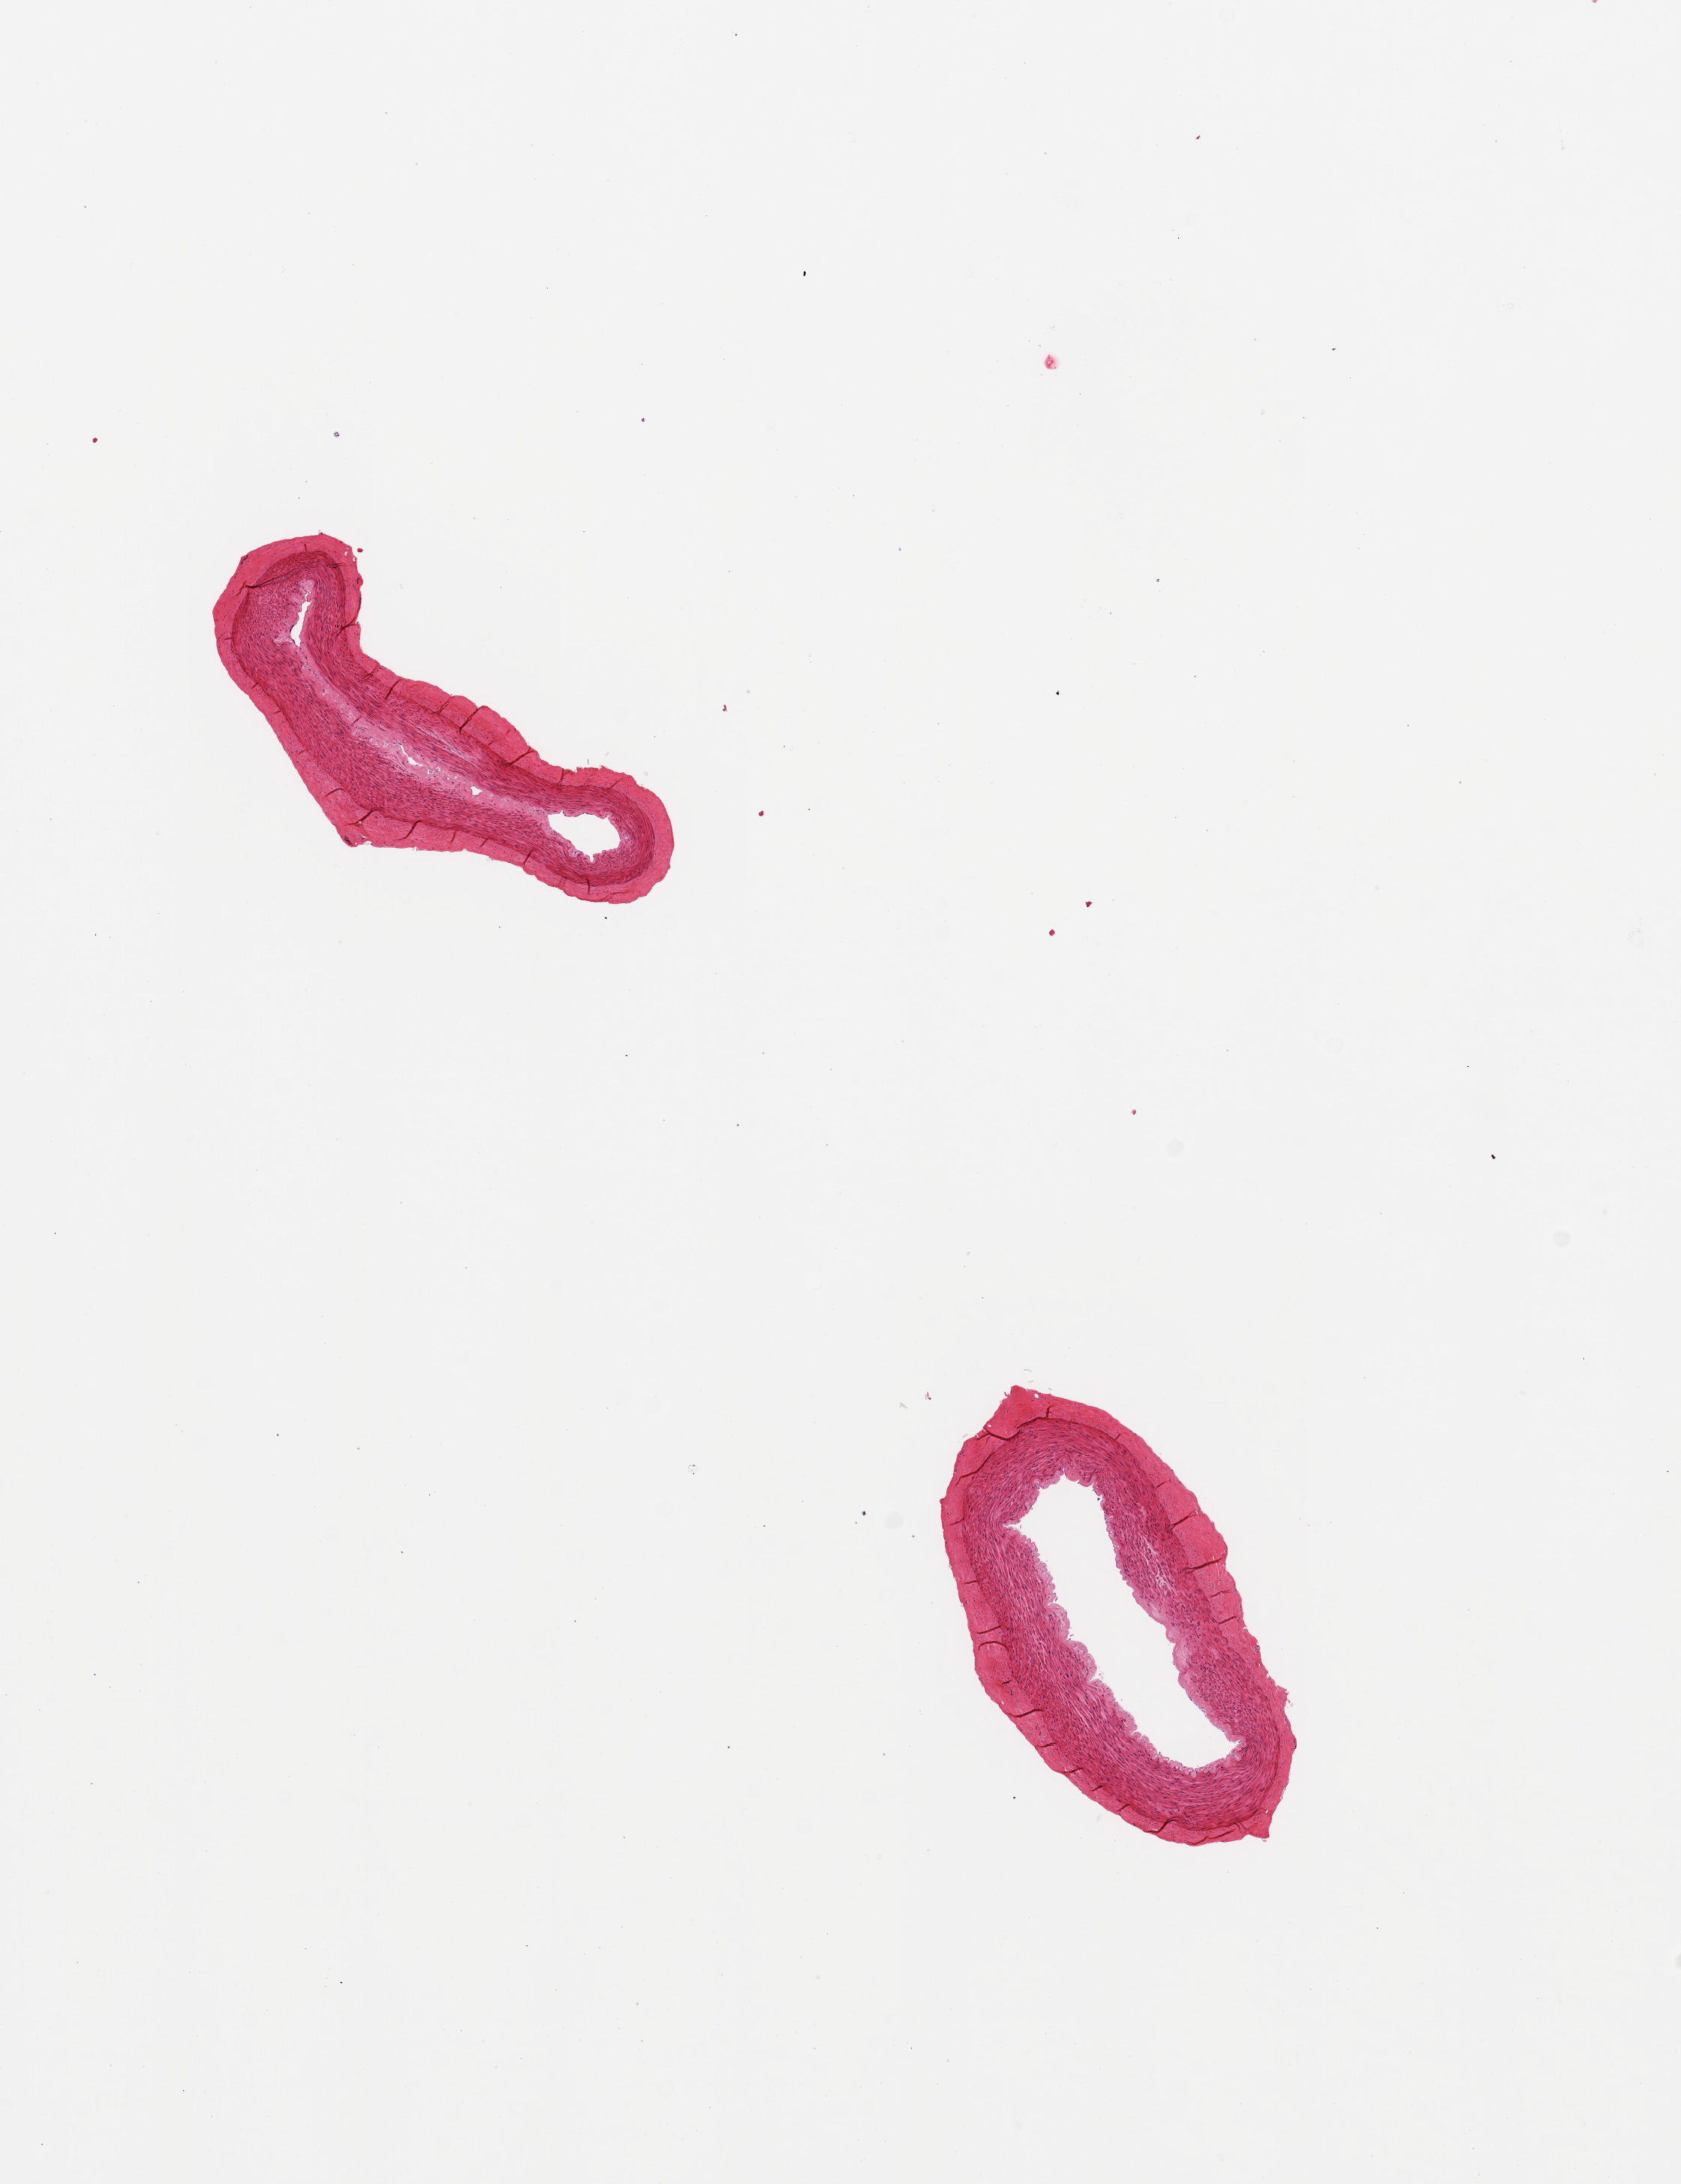
Whole-slide image, hematoxylin and eosin (H&E) stain, low-resolution overview of the scanned area, about 8.9 x 11.5 mm (slide scanned at 20x), PAXgene-fixed, paraffin-embedded tissue, target tissue: tibial artery, tissue donor sample. Donor: female.
Review note (as recorded): 2 pieces, no adherent fat or significant atherosis.